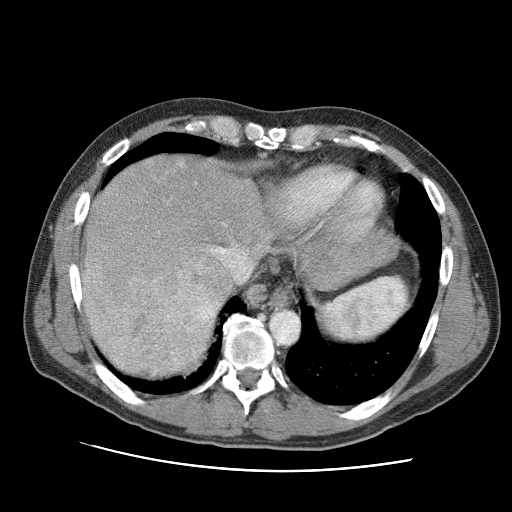
Contrast-enhanced abdominal CT (liver protocol), one axial slice. Slice 80 of 95 in the series (ordered by position). Reconstruction kernel STANDARD. One of 2 acquisitions stored at this slice position. Soft-tissue window (W 400 / L 40 HU). 2.5 mm slice thickness. 512 × 512 image matrix, field of view 360 × 360 mm. From the clinical record (not read from this slice): diagnosis: hepatocellular carcinoma (patient treated with transarterial chemoembolisation; whether this scan precedes or follows treatment is not stated here); TNM stage (as recorded): Stage-IVA; Child-Pugh class: A; tumour differentiation: moderately differentiated.
Outlined on this slice (semi-automatic segmentation, software-assisted and operator-edited):
- liver parenchyma outside the tumour (the mass and vessels are separate outlines, so this box may not span the whole liver): bounding box <80,154,276,313> (left, top, right, bottom; pixels)
- mass: <86,269,219,379>
- liver vessels: <84,164,251,282>